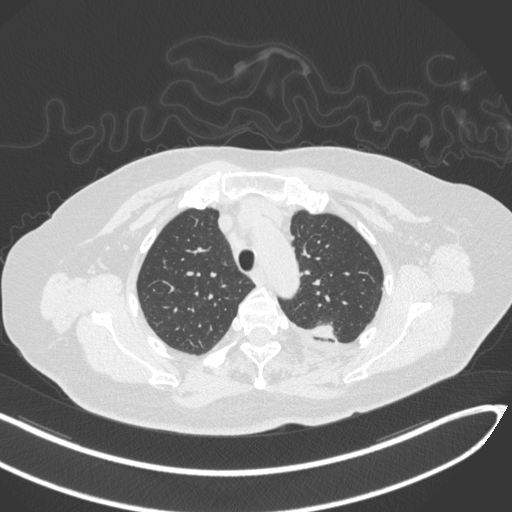
Chest CT, one axial slice. Position 251 of 270 along the scan axis. 120 kVp. Lung window (W 1500 / L -600 HU). 1 mm slice thickness. 512 × 512 image matrix, field of view 400 × 400 mm. Patient: female, 76 years. Case-level facts recorded for this patient, not image findings: clinical TNM (as recorded): T1c N0 M0.
Outlined on this slice (bounding box drawn by a radiologist):
- lung tumour (recorded histology: adenocarcinoma): bounding box [x1, y1, x2, y2] px = [306, 315, 340, 343]